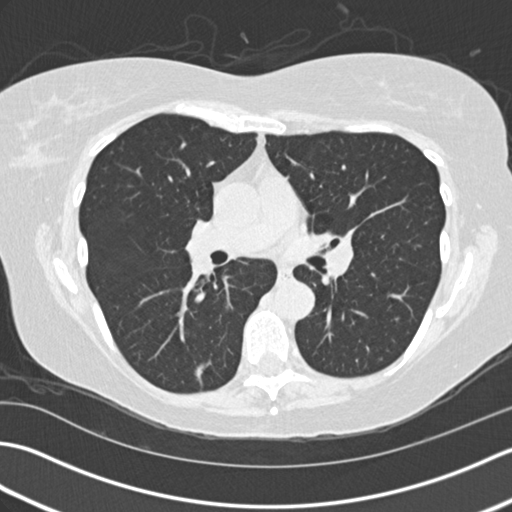
Low-dose screening chest CT, one axial slice; lung window (W 1500 / L -600 HU); 2 mm slice thickness; 512 × 512 image matrix, field of view 350 × 350 mm.
Outlined on this slice (outlined manually by an expert reader):
- lesion 1 (tumor, lower lobe of right lung): bounding box (x1, y1, x2, y2) in pixels: (196, 362, 212, 384)